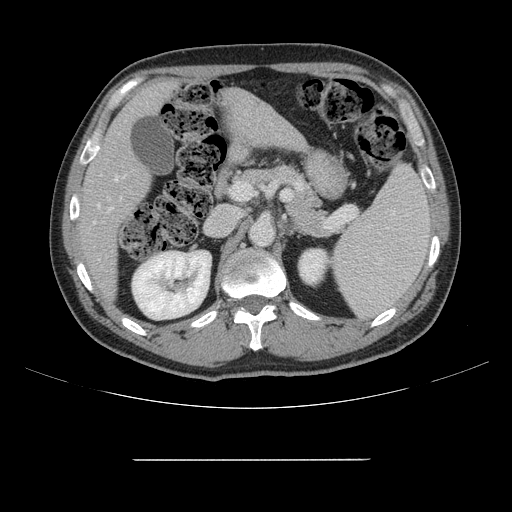
Contrast-enhanced abdominal CT, one axial slice. Position 82 of 164 along the scan axis. Soft-tissue window (W 400 / L 40 HU). 2.5 mm slice thickness. 512 × 512 image matrix, field of view 404 × 404 mm. Male patient, age 54 years. Case-level facts recorded for this patient, not image findings: diagnosis: colorectal cancer liver metastases, imaged before liver resection; multiple liver metastases: yes; largest metastasis: 1 cm.
Annotated regions visible in this slice (manually delineated by an expert):
- hepatic veins: bounding box (x1, y1, x2, y2) in pixels: (97, 175, 118, 208)
- liver: (82, 84, 301, 294)
- planned liver remnant (the part of the liver to remain after resection): (82, 84, 172, 294)
- portal vein (with intrahepatic branches): (108, 208, 112, 212)